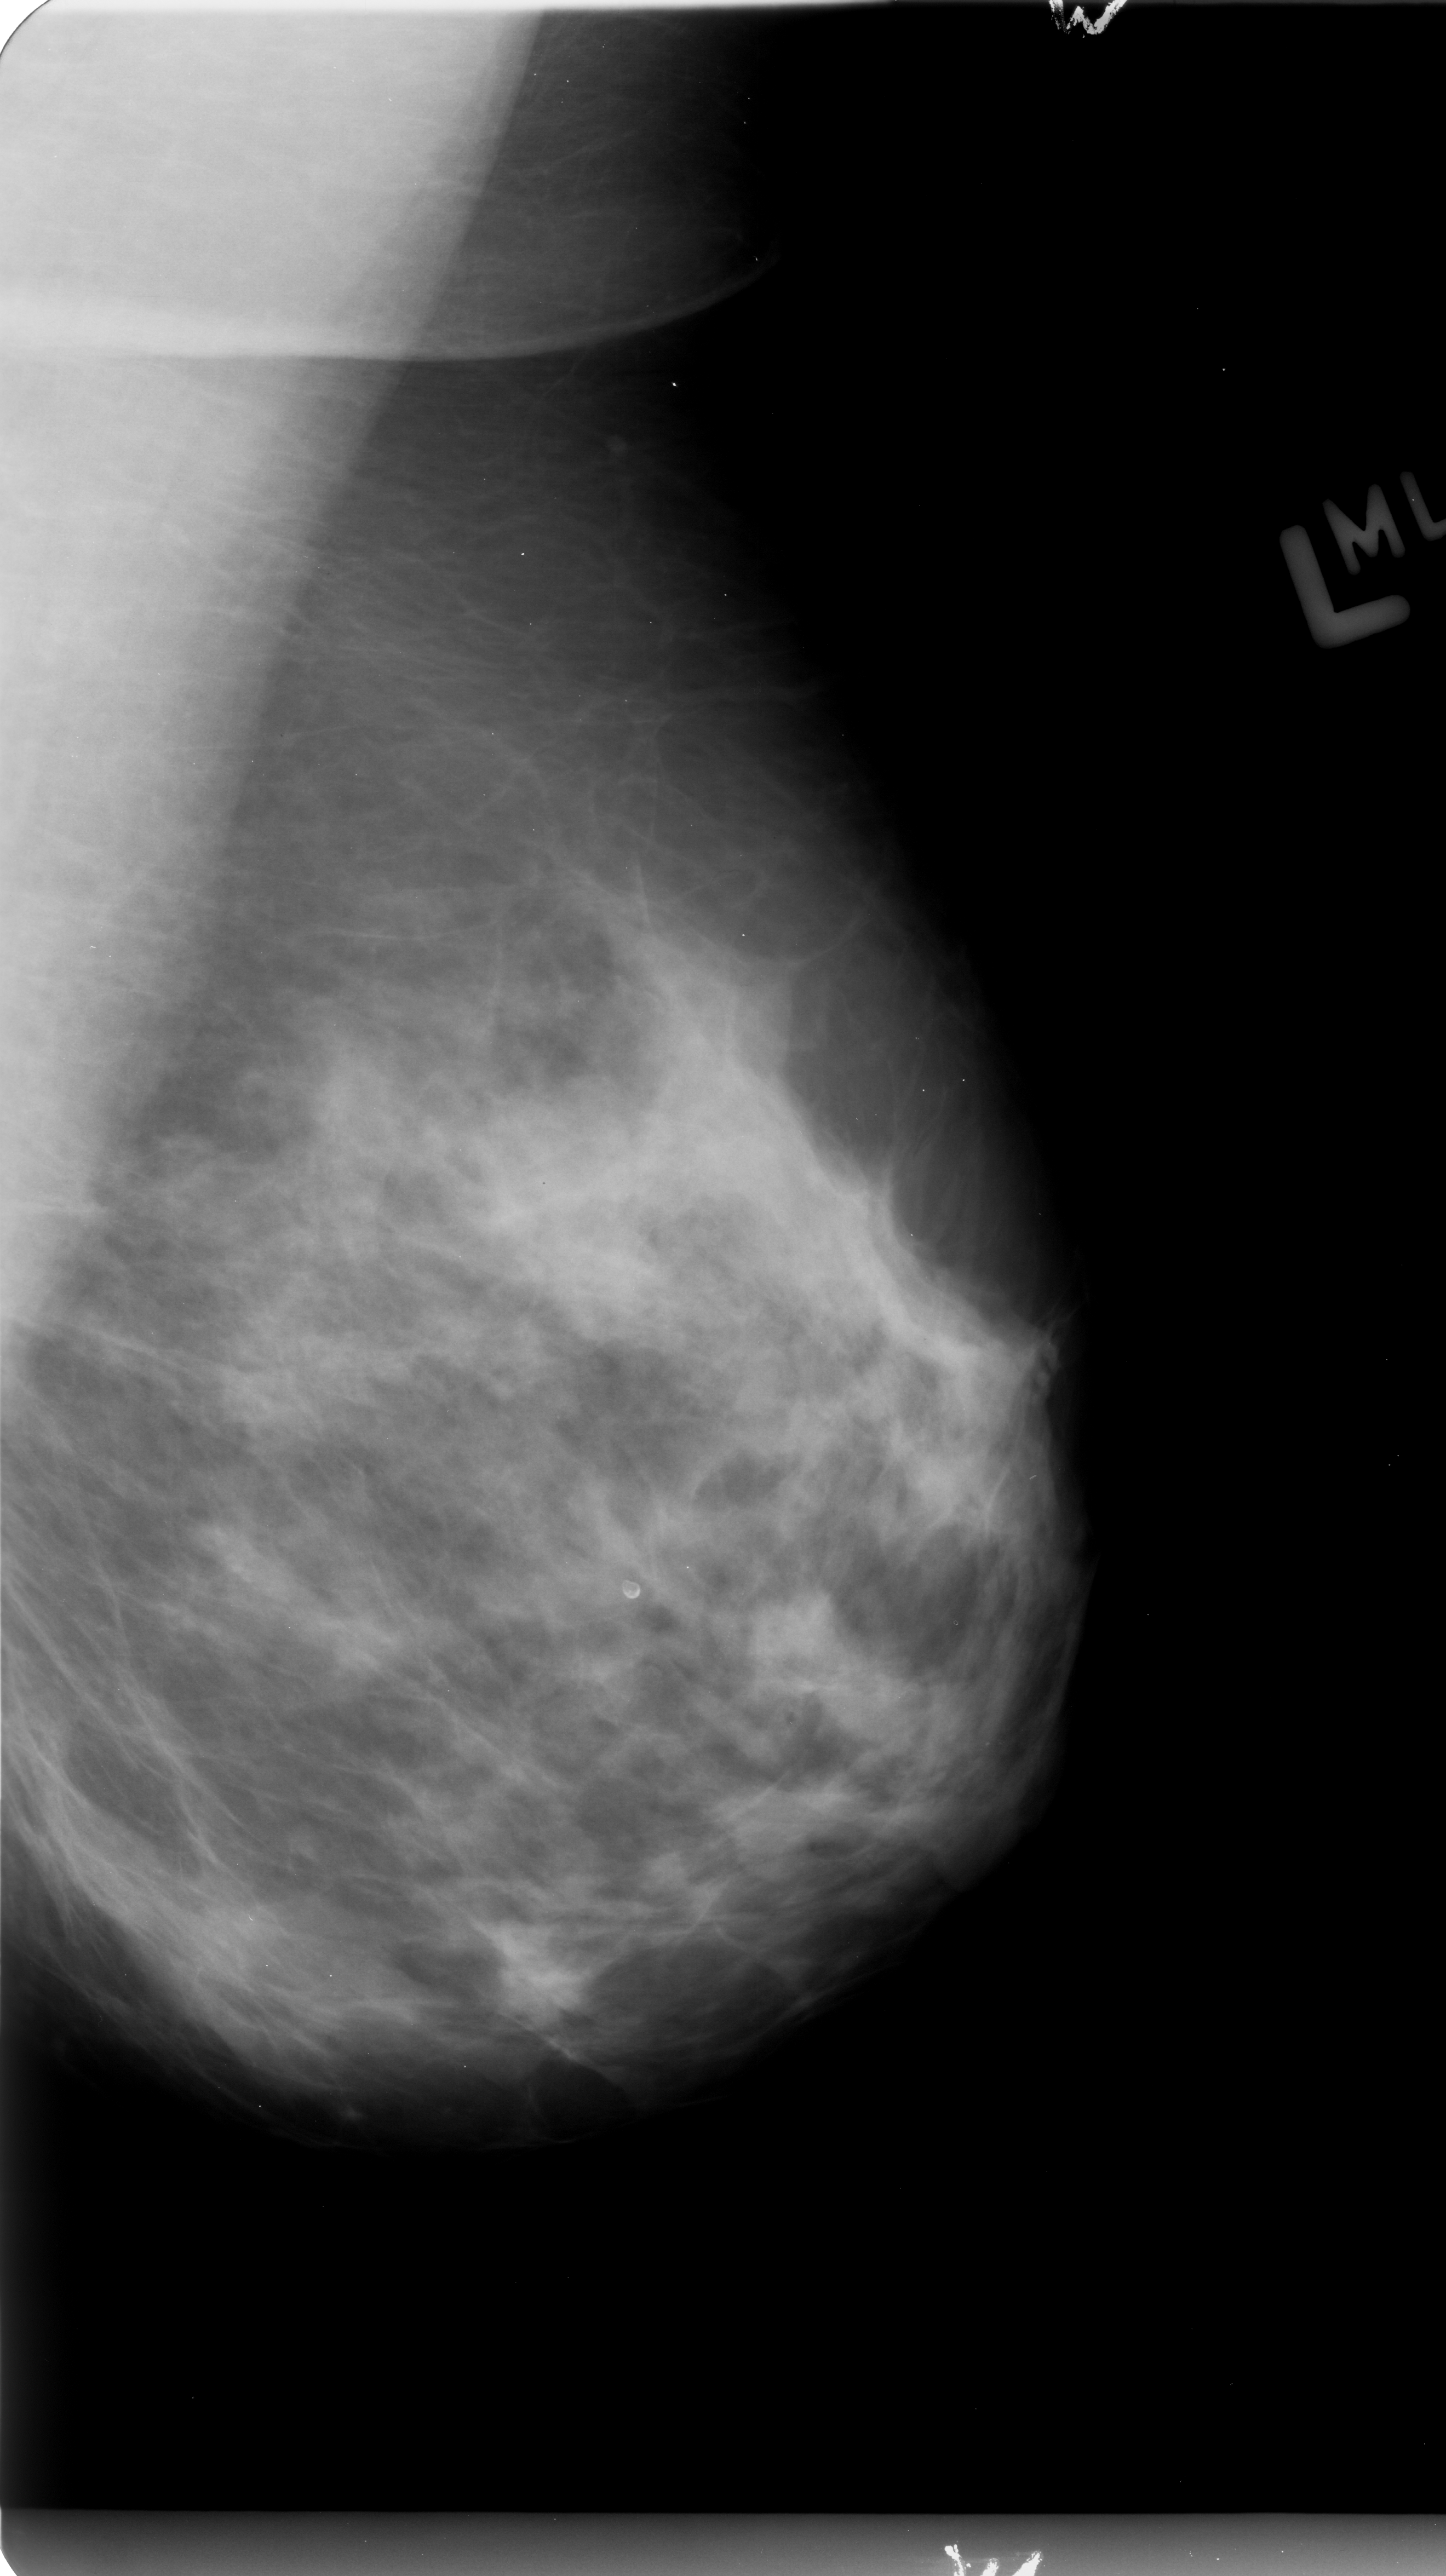
Mammogram (digitized film). Left breast. Mediolateral oblique (MLO) view. BI-RADS breast density category 3 (scale 1–4). 1446 × 2576 image matrix.
Marked abnormalities (boxes around the expert regions of interest):
- calcifications, morphology punctate / pleomorphic, distribution clustered; BI-RADS assessment category 4; subtlety rating 2 on a 1 (subtle) to 5 (obvious) scale; pathology (as recorded): benign: bounding box (x1, y1, x2, y2) in pixels: (446, 928, 882, 1328)